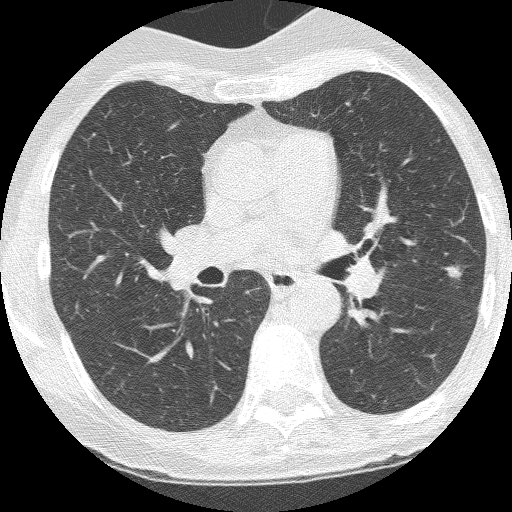
Low-dose screening chest CT, axial slice; third screening round (two years after baseline); lung window (W 1500 / L -600 HU). Female participant, aged 60 years at enrolment. Current smoker at enrolment.
Expert-annotated lung lesion, box from (x=434, y=256) to (x=472, y=294) px. The screening reader recorded 2 non-calcified nodules or masses ≥4 mm on this exam; which of them this box marks is not recorded. Participant outcome: lung cancer diagnosed 37 days after this screen — adenocarcinoma, NOS, left upper lobe, moderately differentiated (G2), stage IA (AJCC 6th edition), 6 mm at pathology.